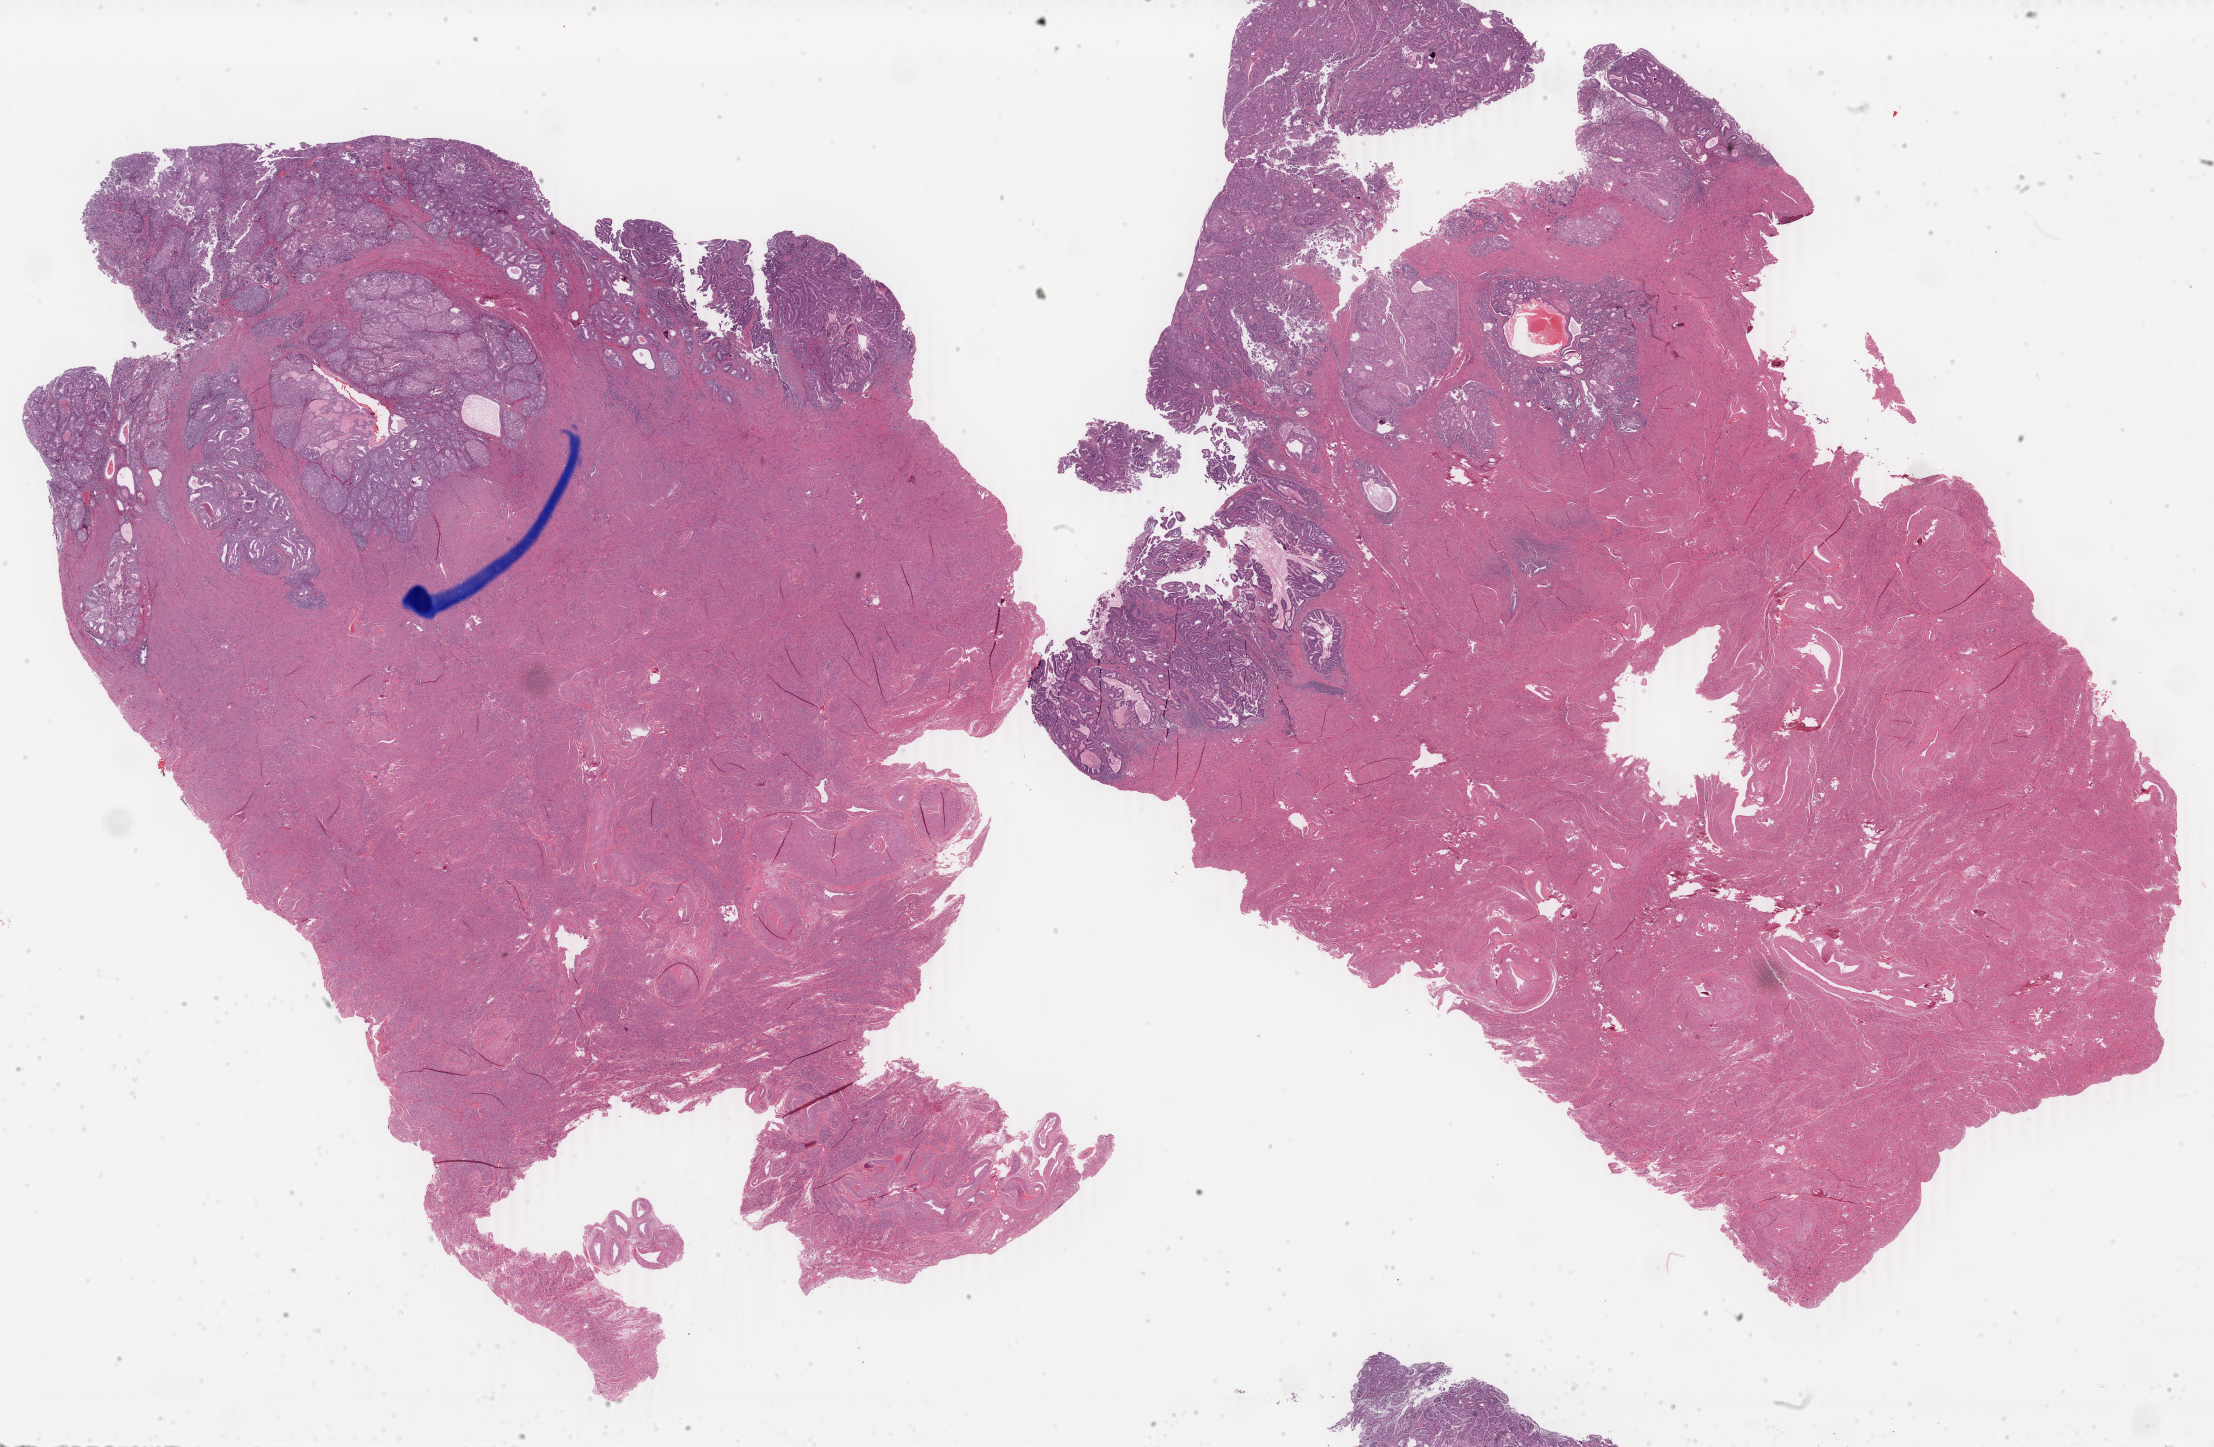
Whole-slide histology image, H&E-stained, whole scanned area (about 35.2 x 23.0 mm, slide scanned at 40x) shown as a low-resolution overview. FFPE section. Primary tumour sample from the uterus. Female patient; age at initial diagnosis 75 years. Histologic grade: G1 (well differentiated).
• pathologic diagnosis: Endometrioid adenocarcinoma, NOS (endometrium)
• FIGO stage: IB